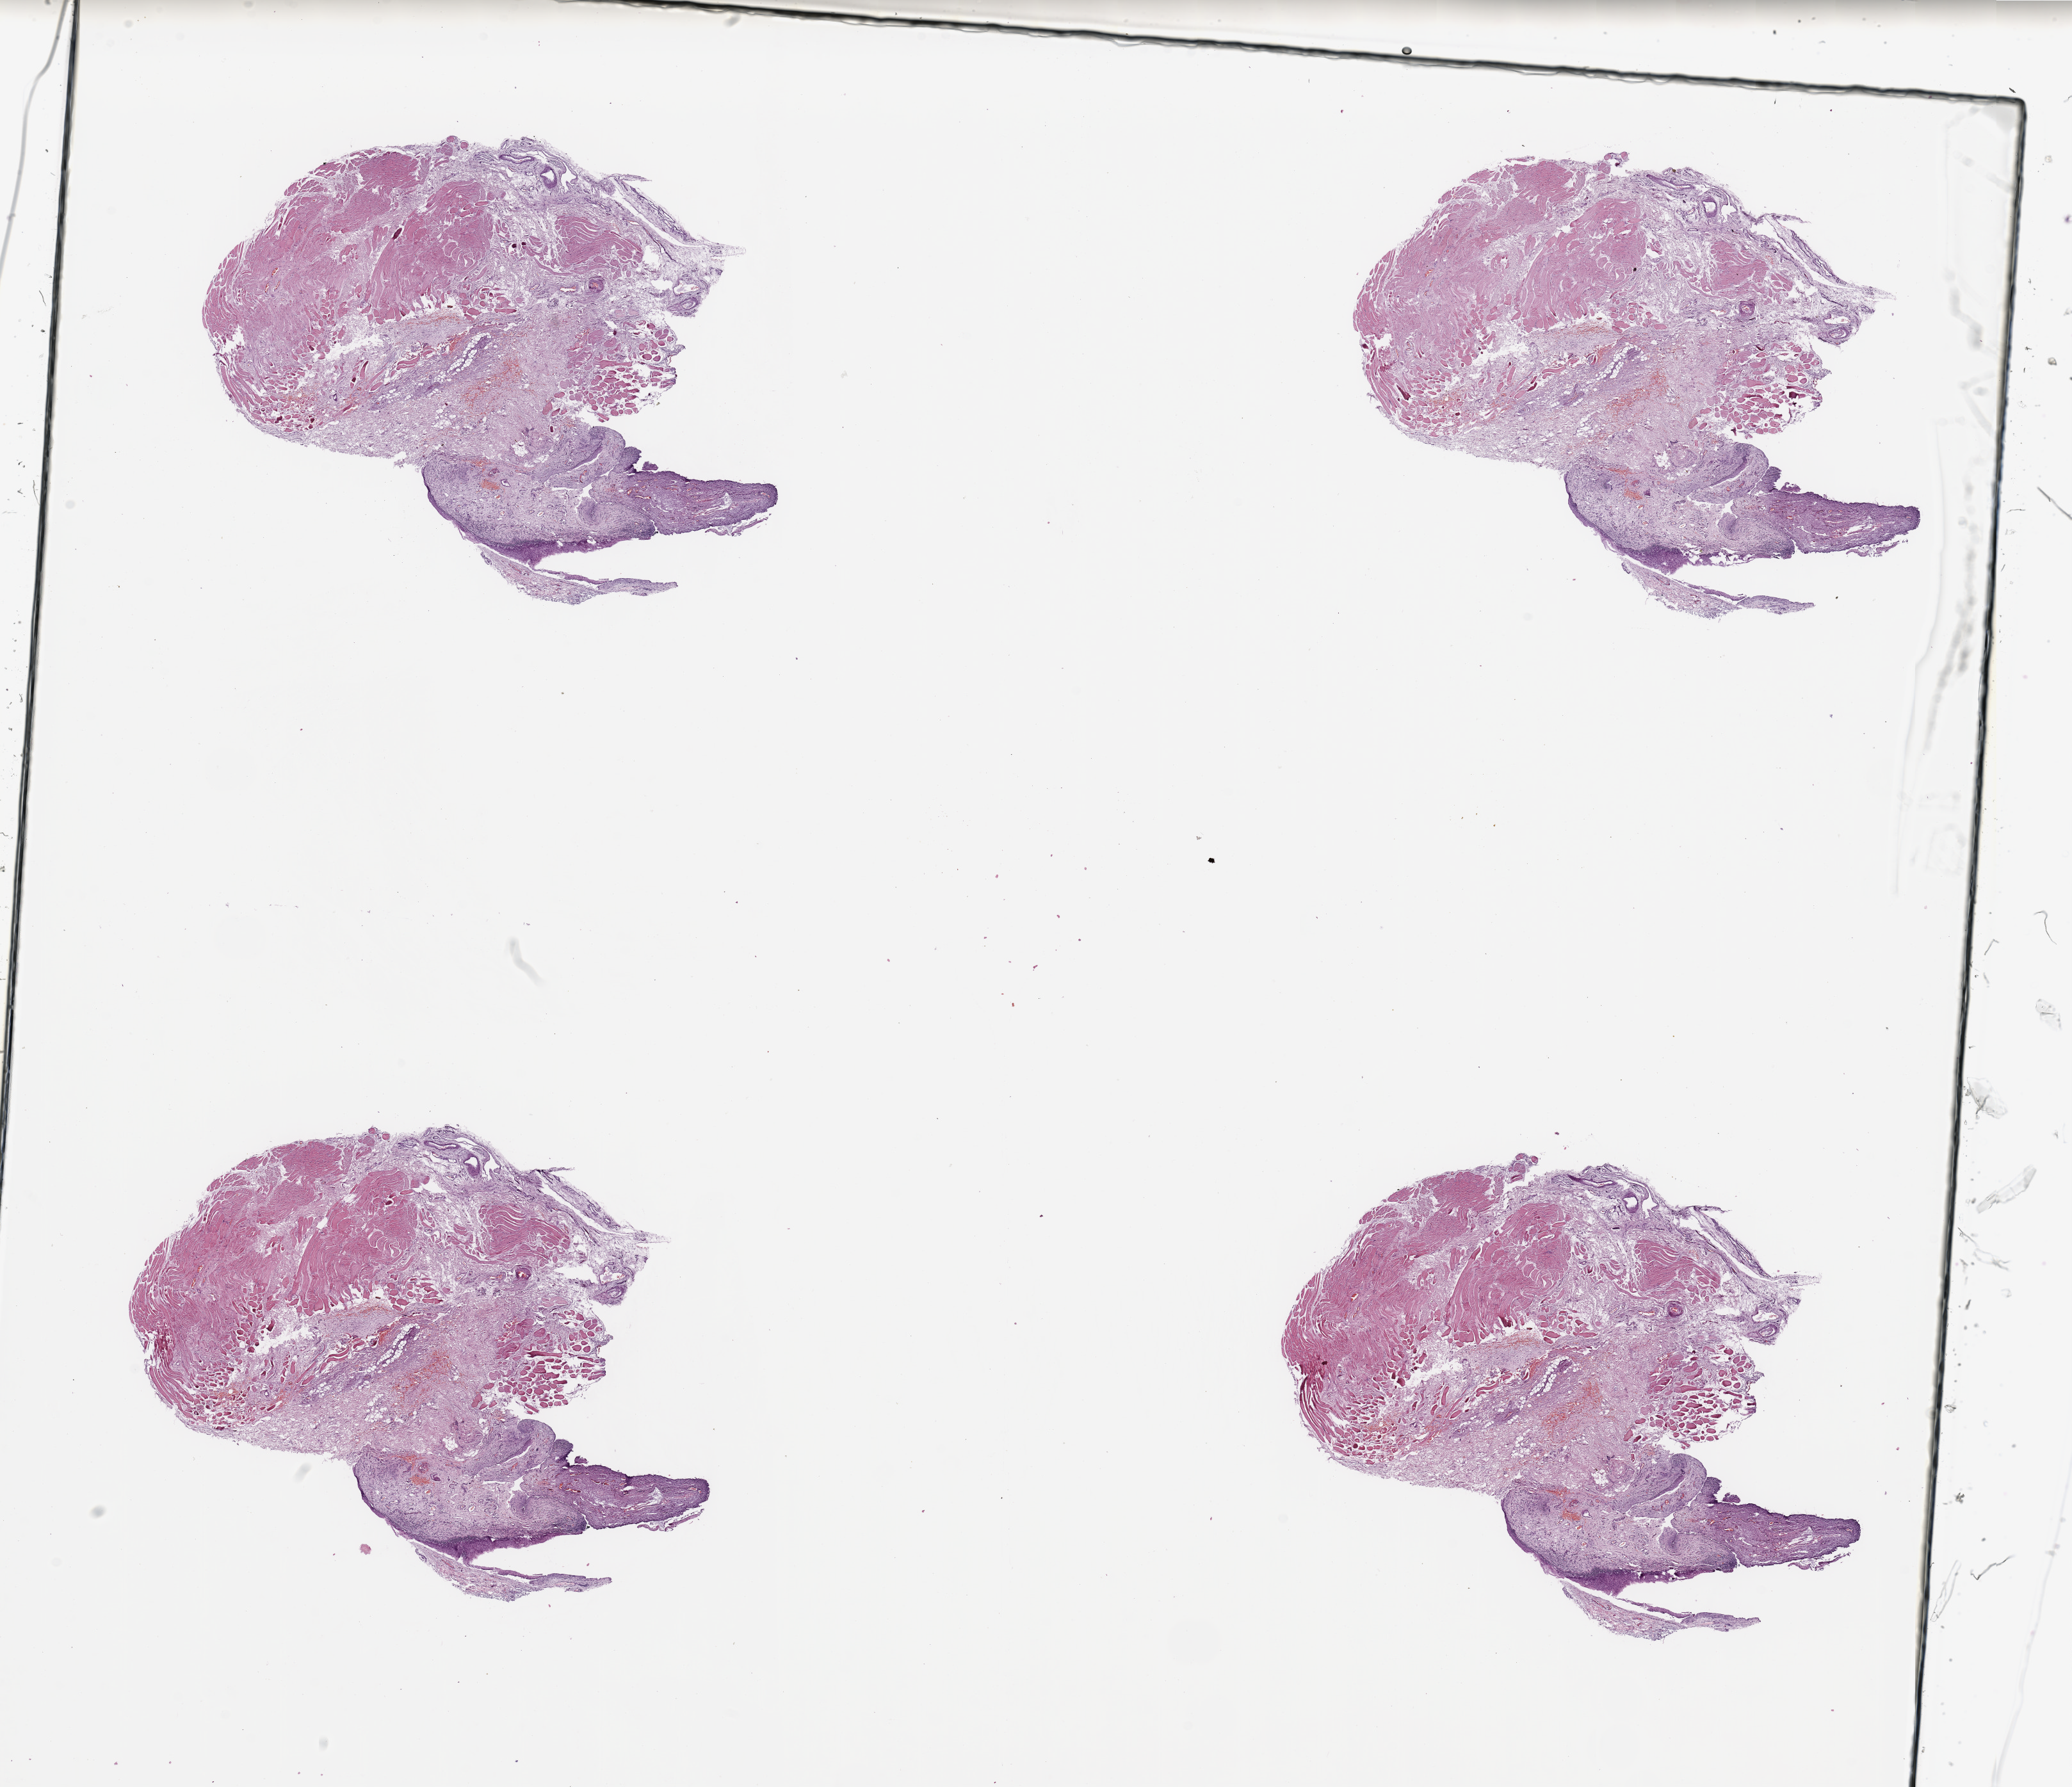
Digitized Hematoxylin and eosin (H&E) stained tissue section (whole slide) — a low-resolution overview of the entire scanned area, about 25.6 x 22.1 mm; normal (non-tumour) tissue sample, sampled site: oropharynx. 53-year-old male patient.
• this section: normal (non-tumour) tissue from the same patient
• patient diagnosis: Squamous cell carcinoma, NOS (oropharynx, NOS)